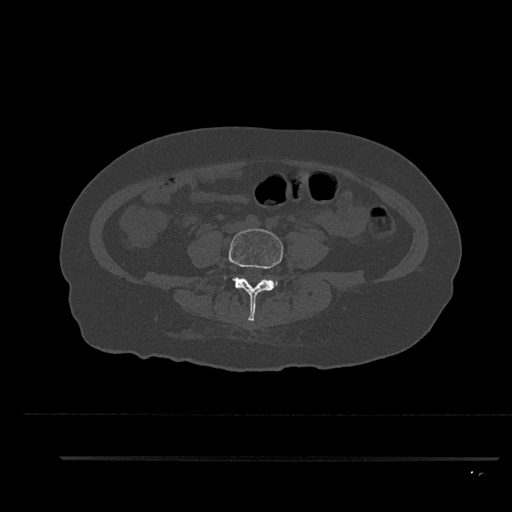
CT including the spine, one axial slice. Slice 11 of 797 in the series (ordered by position). Bone window (W 1800 / L 400 HU). 0.5 mm slice thickness. 512 × 512 image matrix, field of view 408 × 408 mm. Patient: female, 44 years. Case-level facts recorded for this patient, not image findings: primary cancer: renal.
Annotated regions visible in this slice (semi-automatic segmentation, software-assisted and operator-edited):
- L4 vertebra: bounding box (x1, y1, x2, y2) in pixels: (228, 228, 284, 321)